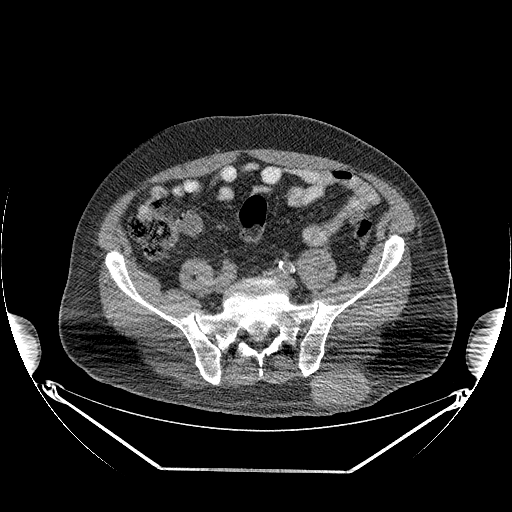
CT of an extremity soft-tissue mass (from a PET/CT study), one axial slice. Position 90 of 267 along the scan axis. Soft-tissue window (W 400 / L 40 HU). 3.75 mm slice thickness. 512 × 512 image matrix, field of view 500 × 500 mm. Male patient. Case-level facts recorded for this patient, not image findings: histological type: pleiomorphic leiomyosarcoma; grade: high; site of the primary tumour: left buttock.
Outlined on this slice (expert contour drawn on MRI and transferred to this co-registered scan by the dataset authors):
- gross tumour volume including surrounding oedema: bounding box (x1, y1, x2, y2) in pixels: (311, 367, 369, 408)
- gross tumour volume (mass): (311, 370, 366, 408)